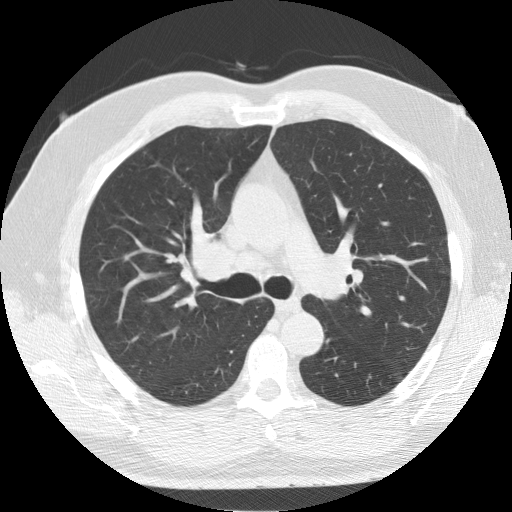
Low-dose screening chest CT, axial slice; second screening round (one year after baseline); lung window (W 1500 / L -600 HU). Male participant, aged 64 years at enrolment. Former smoker at enrolment.
- Expert reader's lesion annotation, bounding box (x1, y1, x2, y2) in pixels: (170, 225, 255, 304).
- Reader record for this screening exam (exam-level; its link to the box is not recorded): non-calcified nodule or mass ≥4 mm, right lower lobe, 7 × 5 mm, smooth margins, soft tissue attenuation, pre-existing on the prior screen: yes; interval growth: no.
- Lung cancer was diagnosed 63 days after this screen: adenocarcinoma, NOS, right upper lobe, poorly differentiated (G3), stage IB (AJCC 6th edition), 37 mm at pathology.